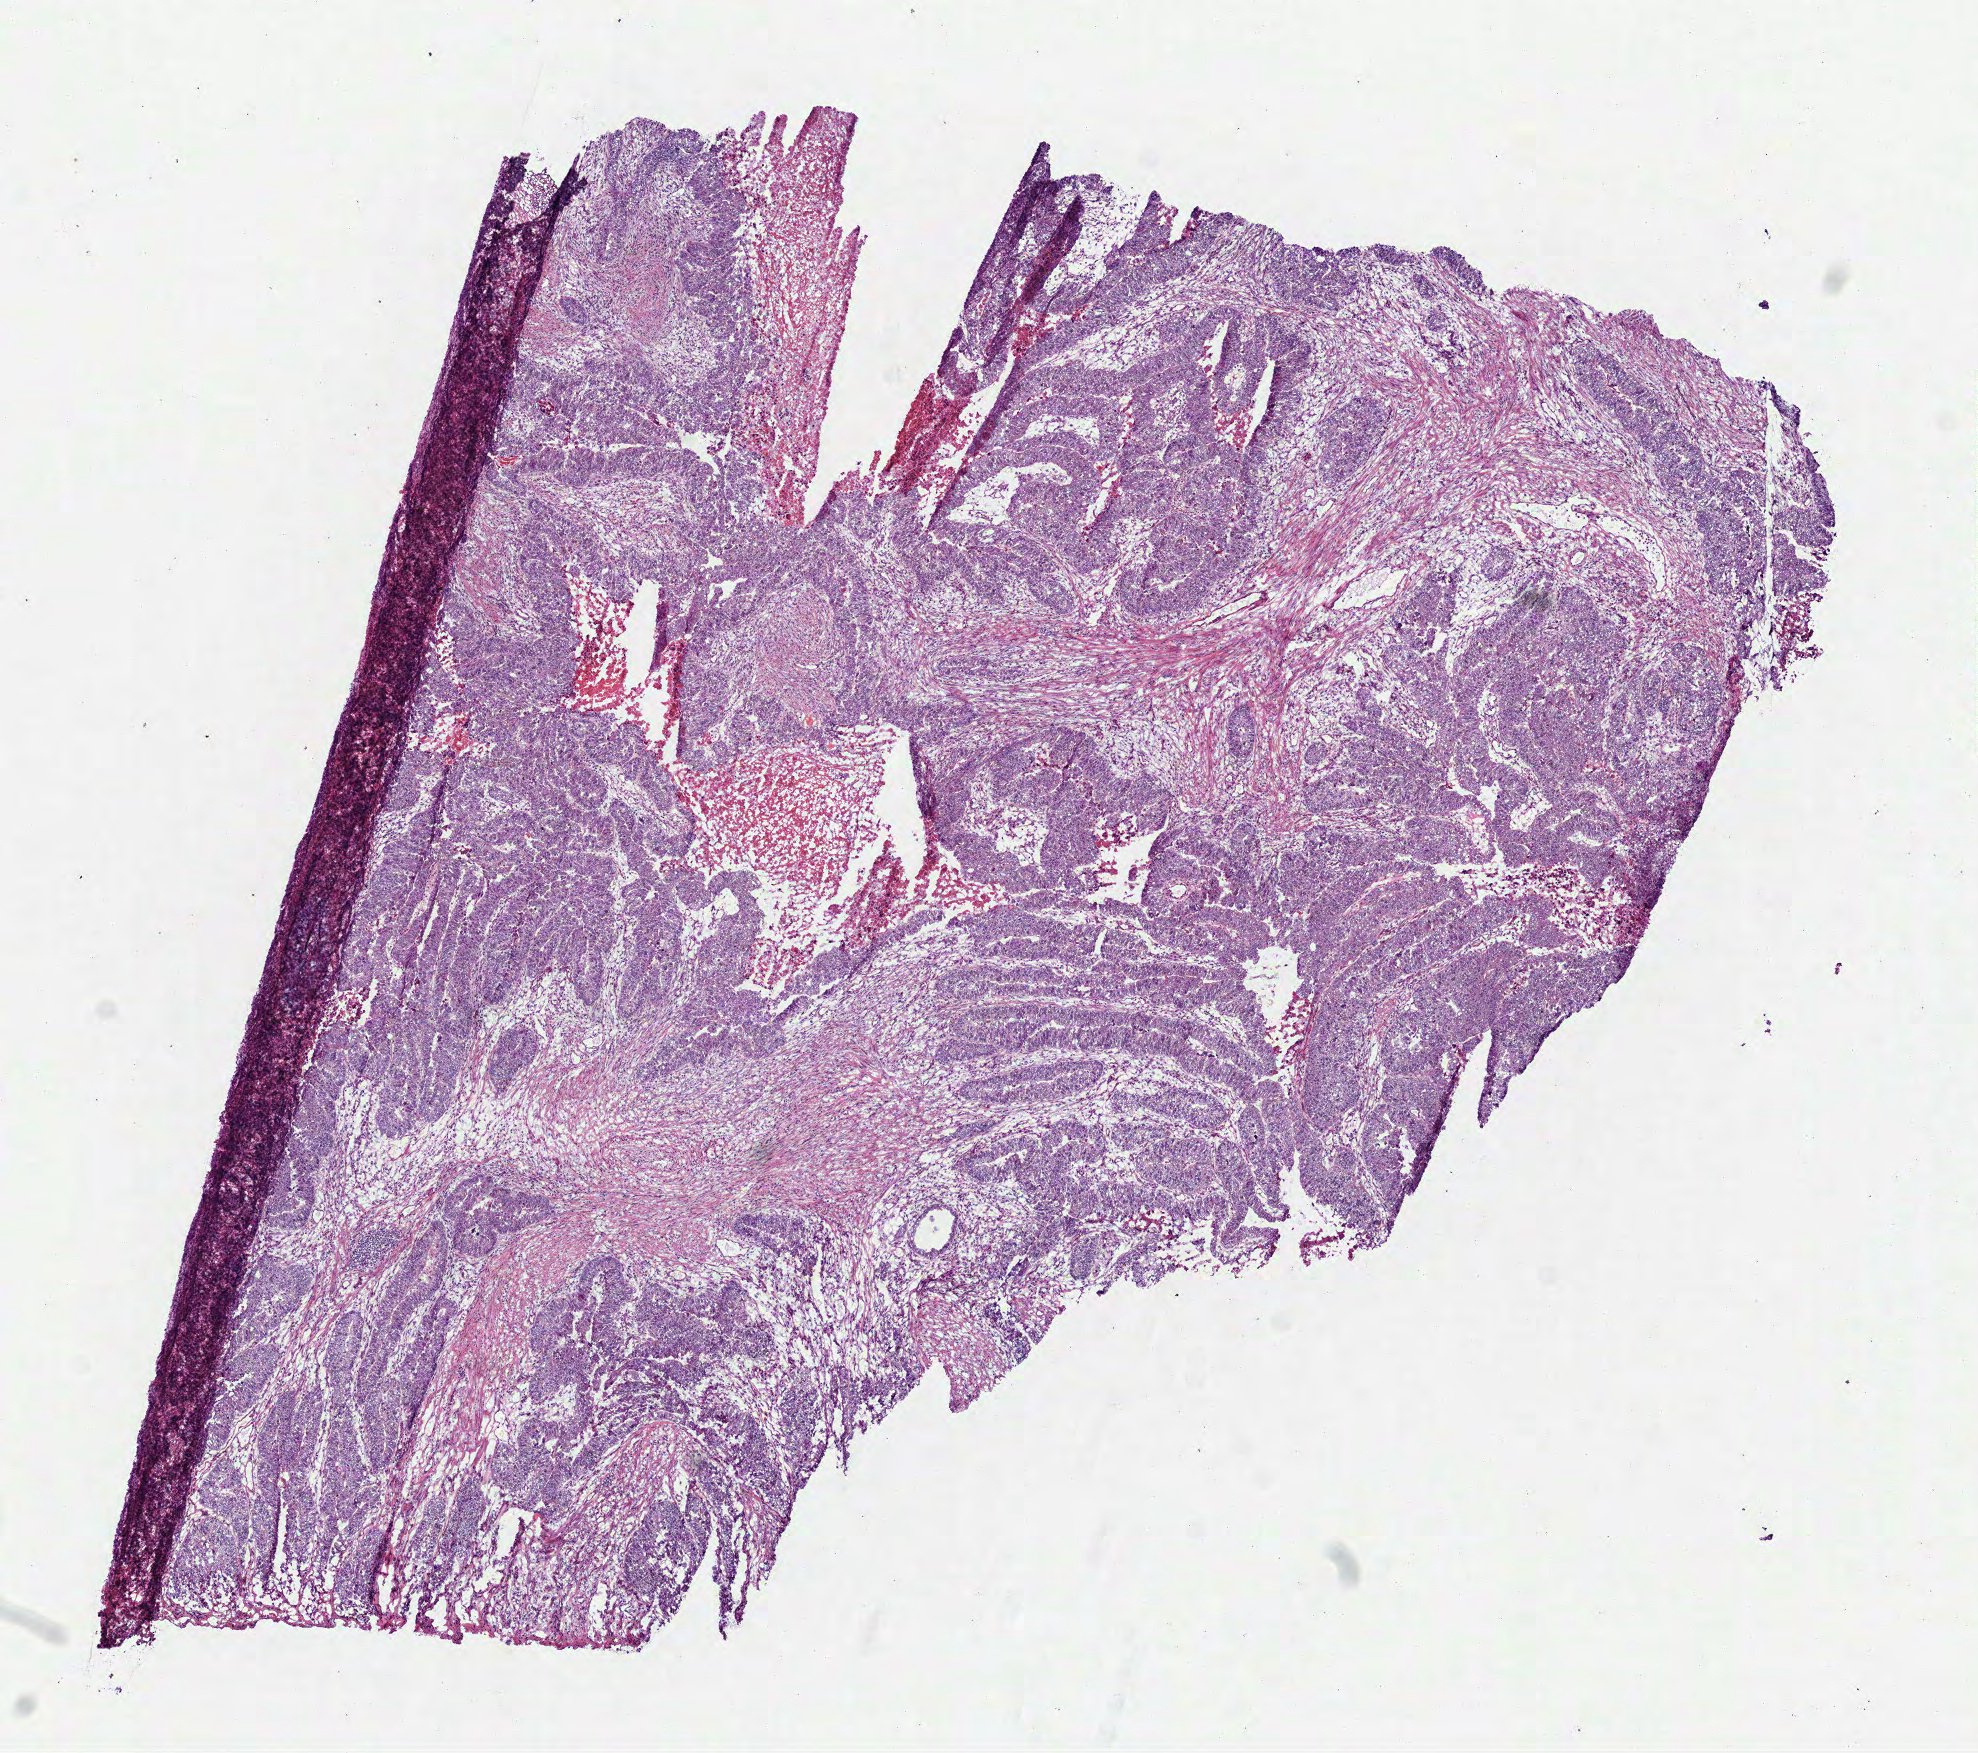
Whole-slide histology image, Hematoxylin and eosin (H&E) stained, shown as a low-resolution overview of the whole scanned area (about 8.0 x 7.1 mm, slide scanned at 40x), frozen section, sample: primary tumour, rectum. Patient: male, age at initial diagnosis 66 years.
Diagnosis: Adenocarcinoma, NOS.